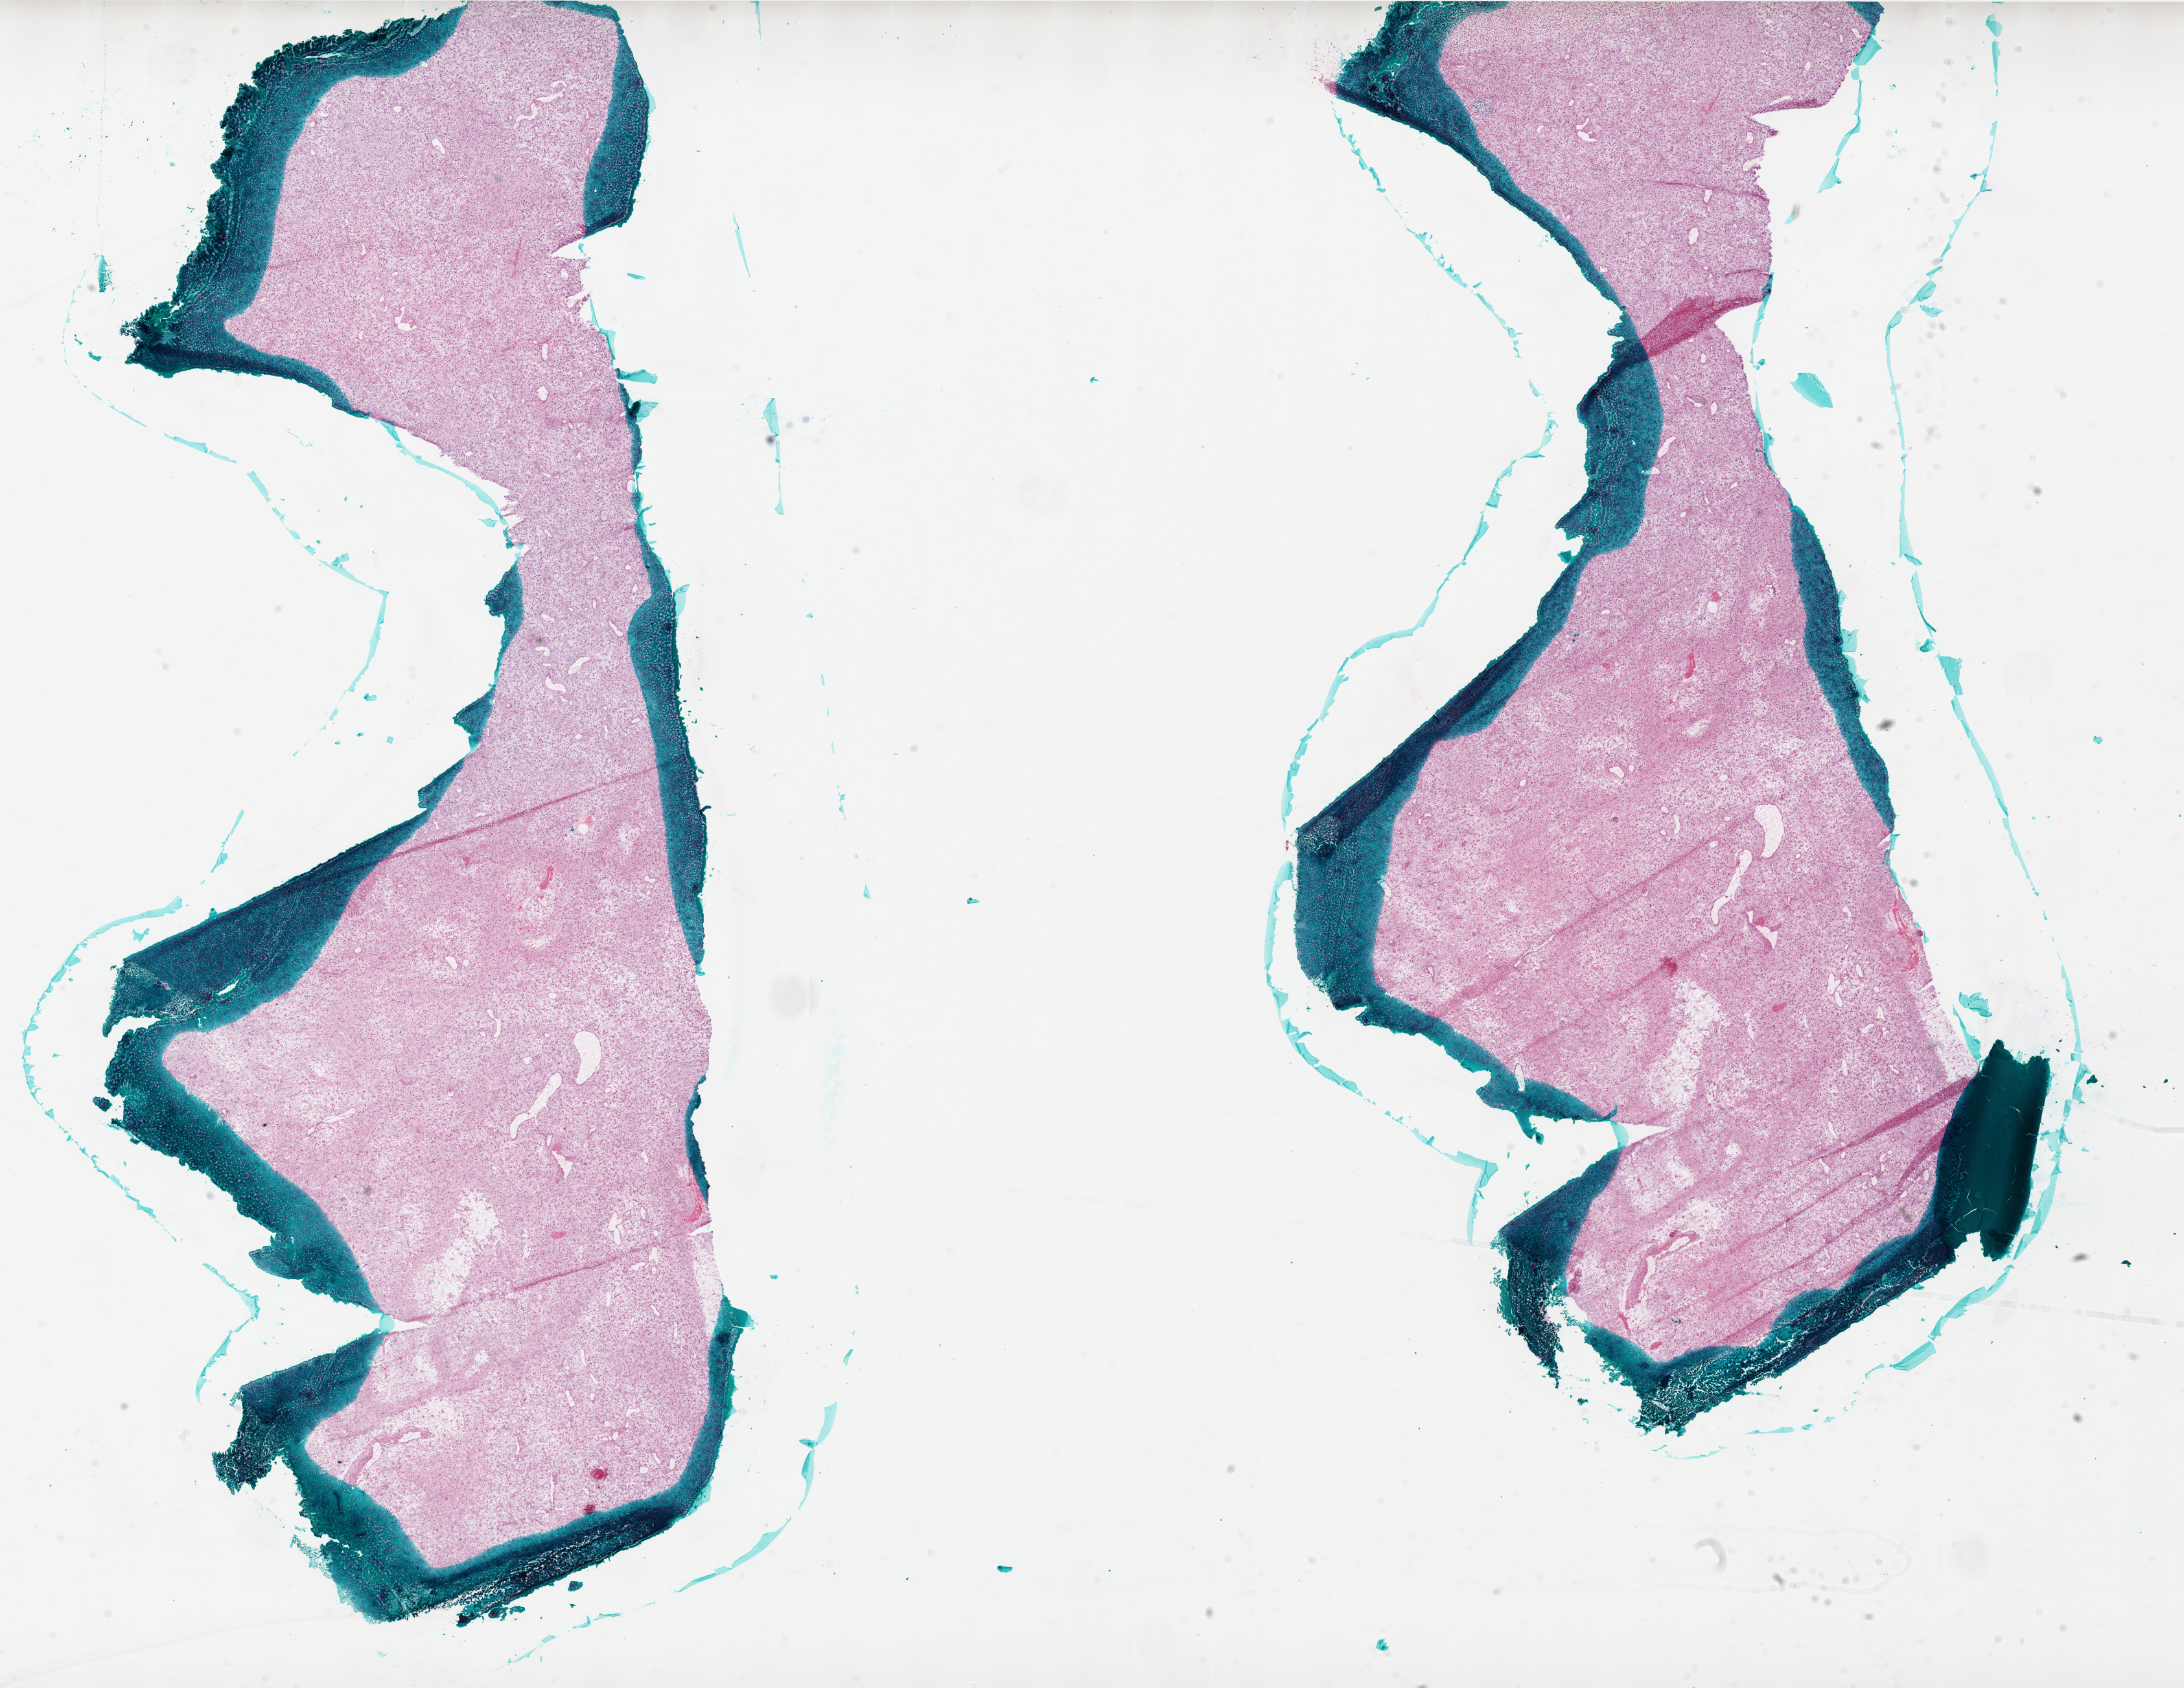
Whole-slide histology image, H&E-stained — low-resolution overview of the scanned area, about 27.0 x 20.8 mm (slide scanned at 20x), frozen section from the bottom of the tissue portion, brain, primary tumour sample. Female patient; age at initial diagnosis 48 years. Slide review estimates, as recorded: tumour cells 80%, tumour nuclei 100%, normal cells 0%, stromal cells 0%, necrosis 20%.
Diagnosis: Glioblastoma.